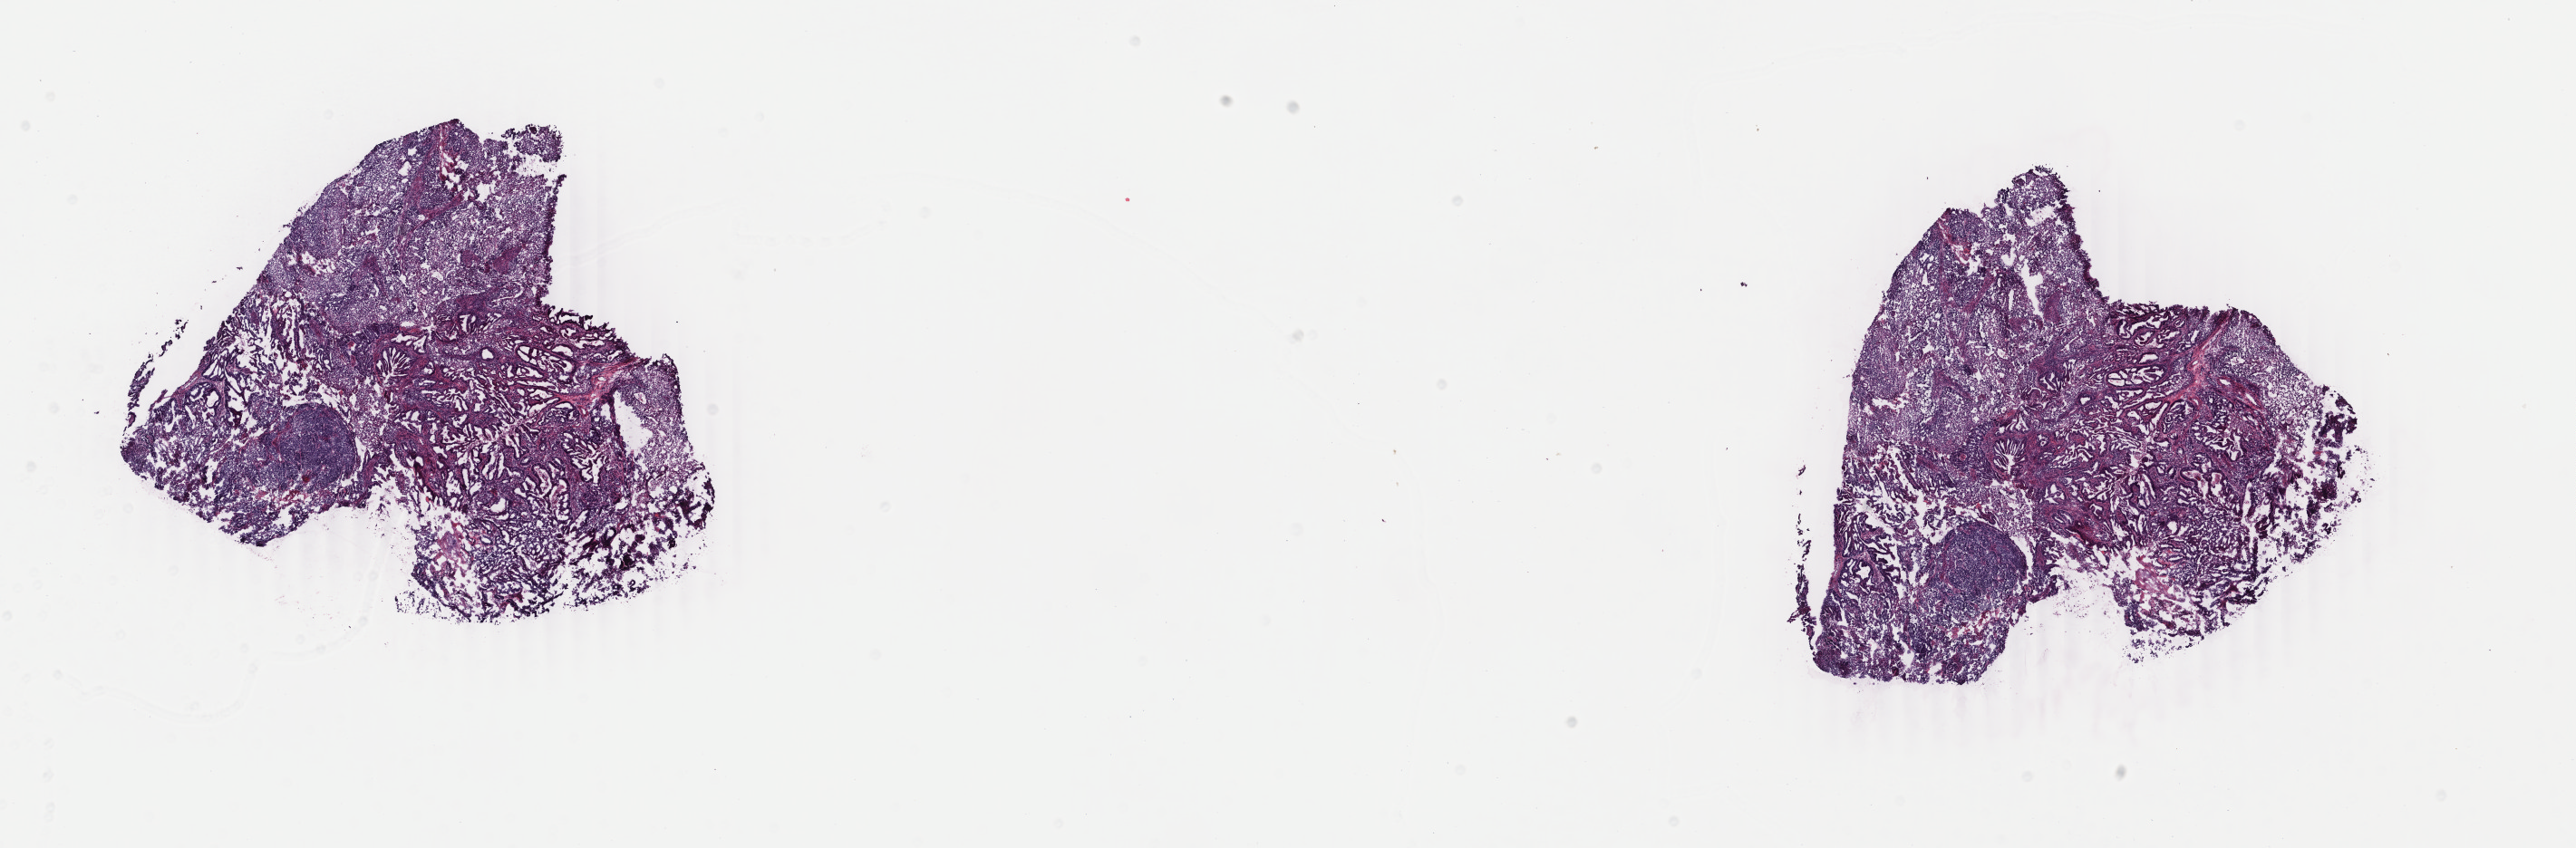
Whole-slide histology image, H&E-stained, shown as a low-resolution overview of the whole scanned area (about 22.6 x 7.4 mm, slide scanned at 40x); frozen section from the bottom of the tissue portion; sample: primary tumour, uterus. Female patient; age at initial diagnosis 59 years. Composition of this section per pathologist review: tumour cells 90%, tumour nuclei 90%.
Diagnosis: Endometrioid adenocarcinoma, NOS (endometrium).